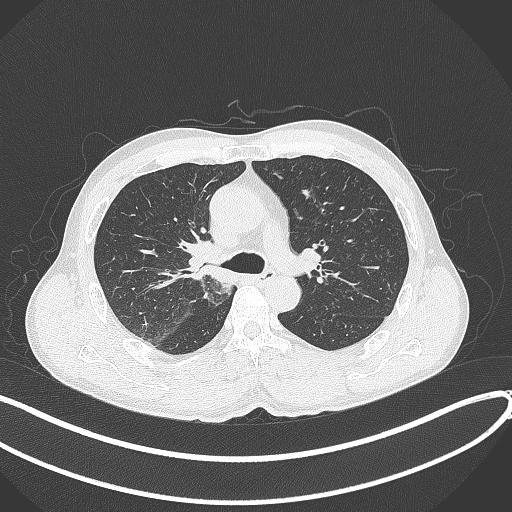
Chest CT, one axial slice. Position 254 of 409 along the scan axis. Lung window (W 1500 / L -600 HU). 1 mm slice thickness. 512 × 512 image matrix, field of view 400 × 400 mm. Male patient, age 53 years. Case-level facts recorded for this patient, not image findings: clinical TNM (as recorded): T1b N0 M0.
Structures marked on this image (rectangle marked by the reading radiologist):
- lung tumour (recorded histology: squamous cell carcinoma): bounding box (x1, y1, x2, y2) in pixels: (179, 236, 226, 284)